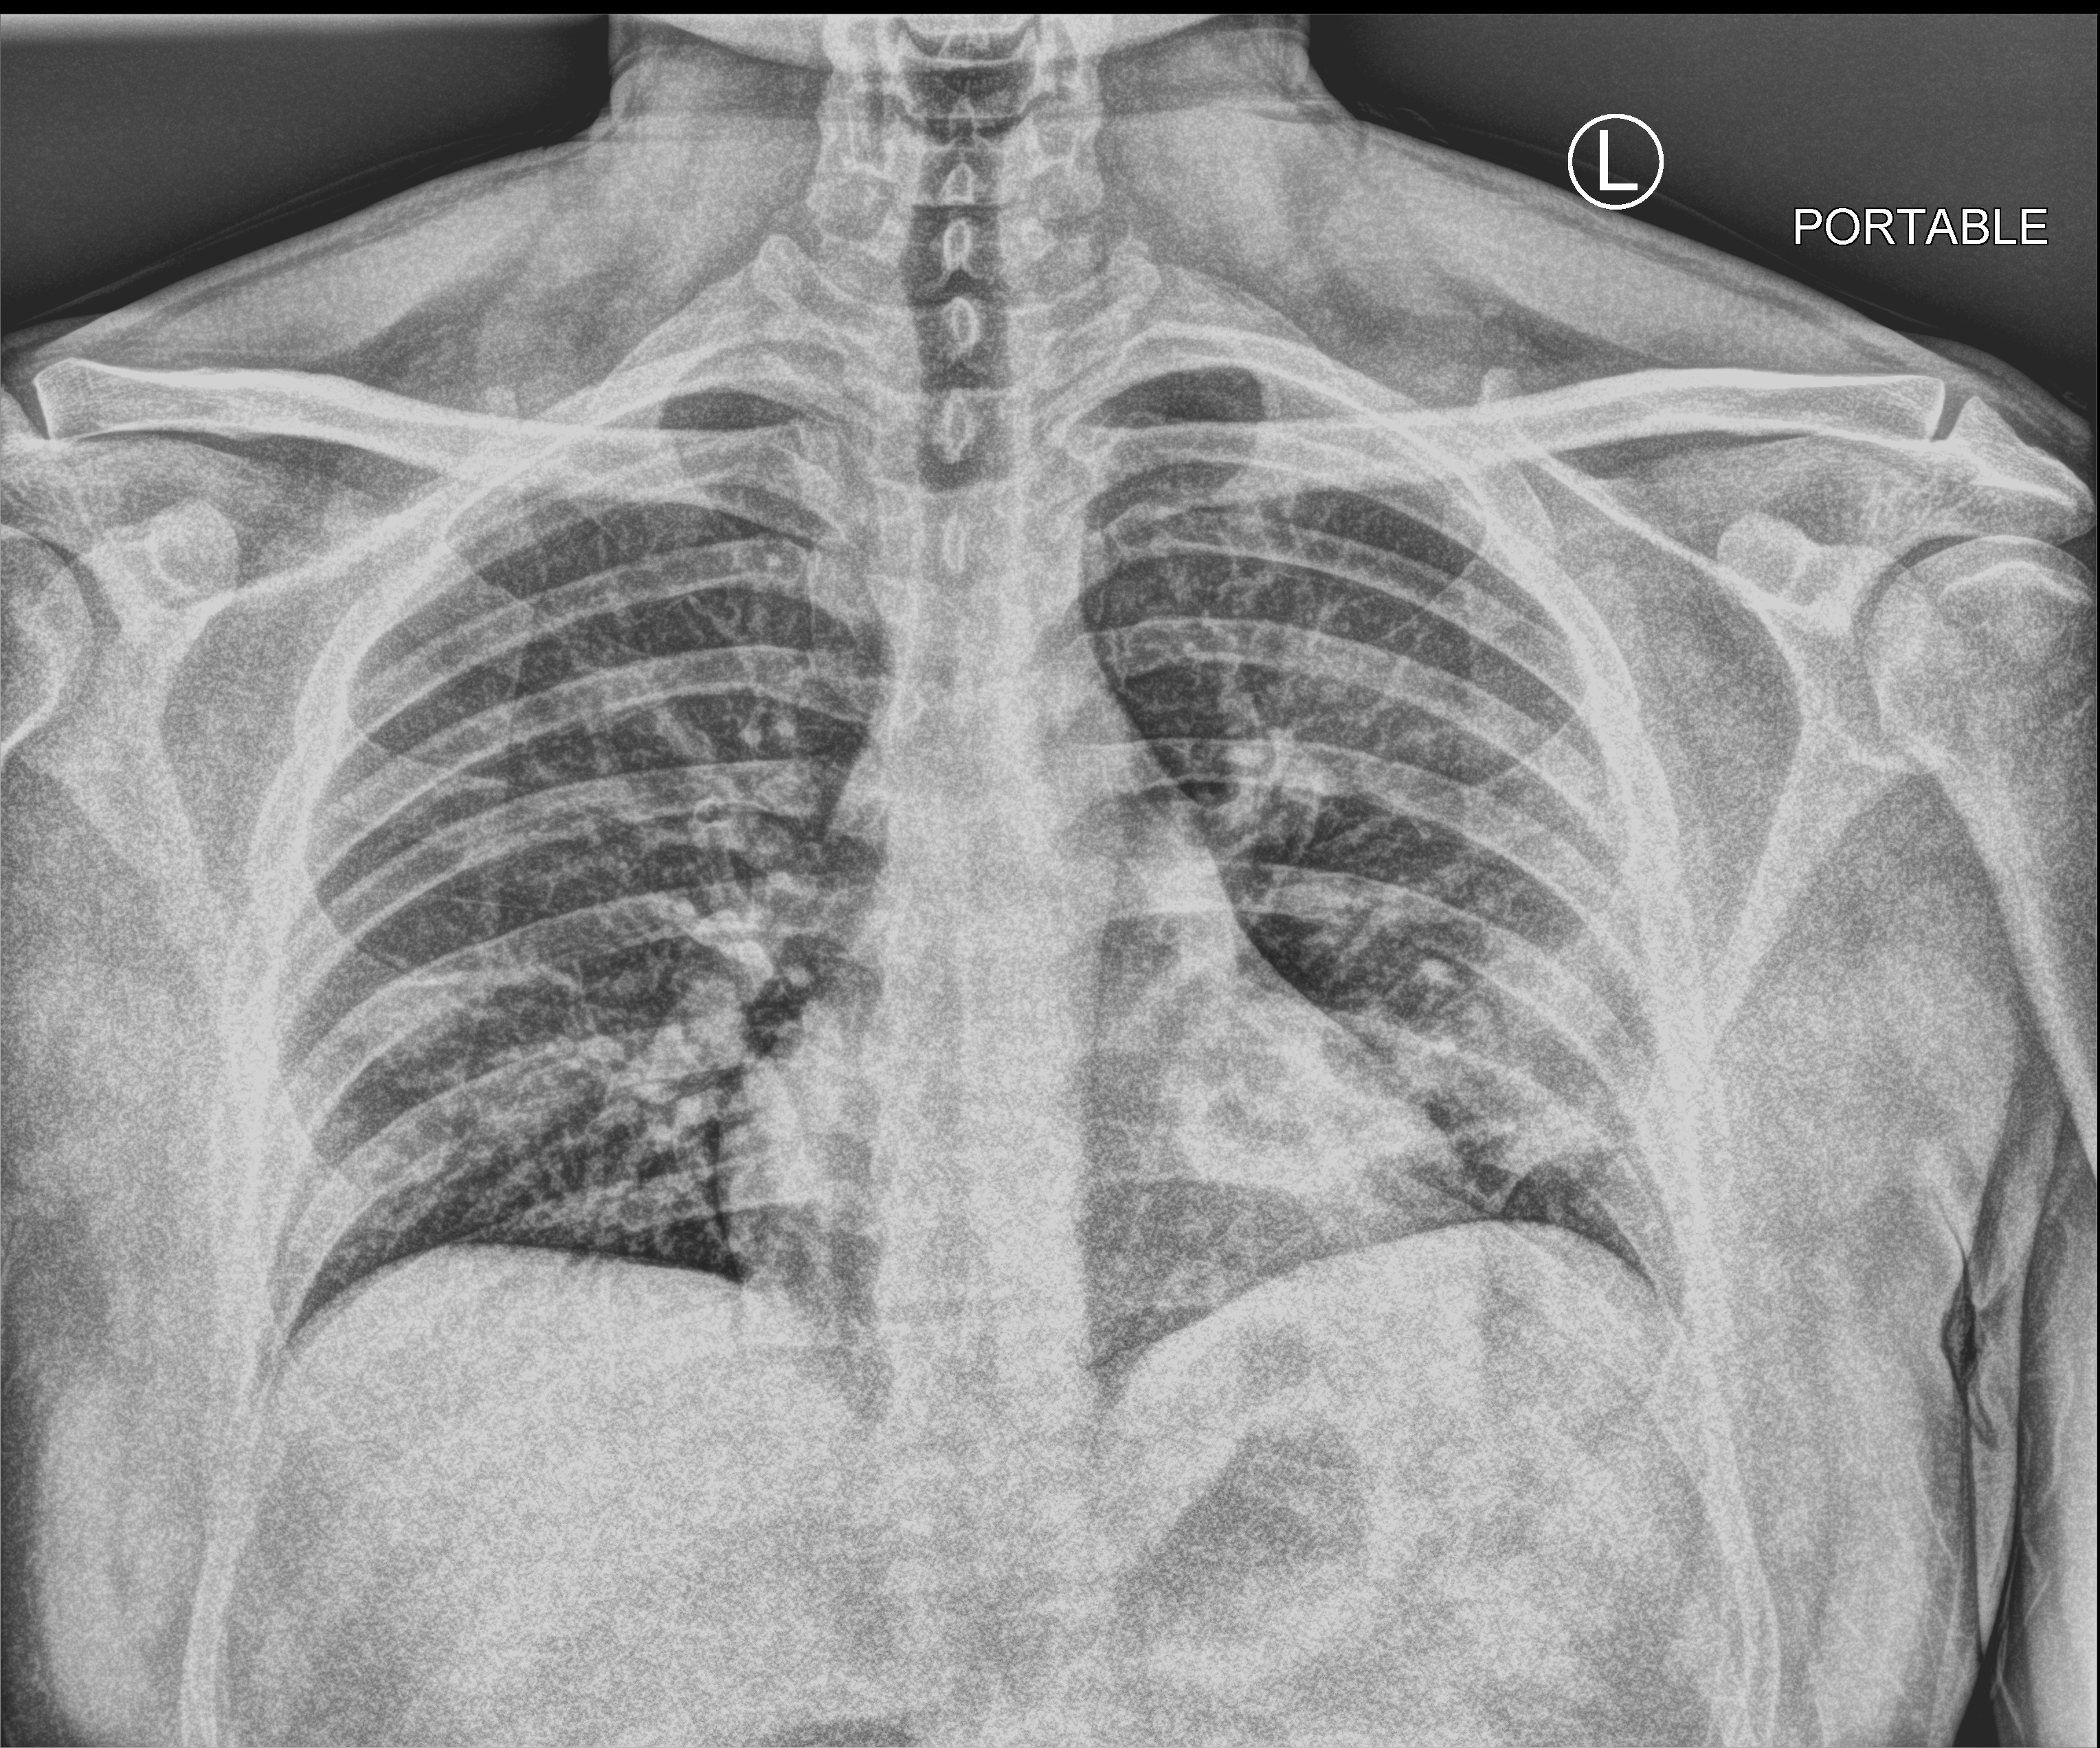
Portable chest radiograph, anteroposterior (AP) projection. Male patient hospitalised with COVID-19, age 18–59 years.
Hospital-stay facts (about this admission, not read from this image; timing relative to this image not recorded):
- mechanically ventilated during this hospital stay: no
- length of hospital stay: 1 day
- admitted to intensive care during this hospital stay: no